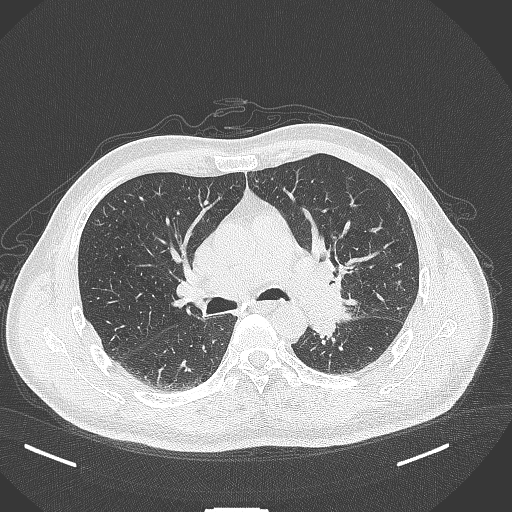
Chest CT, one axial slice. Reconstruction kernel B70f. 120 kVp. Lung window (W 1500 / L -600 HU). 1 mm slice thickness. 512 × 512 image matrix, field of view 400 × 400 mm. Male patient, age 55 years. Case-level facts recorded for this patient, not image findings: clinical TNM (as recorded): T3 N0 M1c; histopathological grade: G3.
Outlined on this slice (rectangle marked by the reading radiologist):
- lung tumour (recorded histology: adenocarcinoma): bounding box [x1, y1, x2, y2] px = [303, 286, 350, 341]